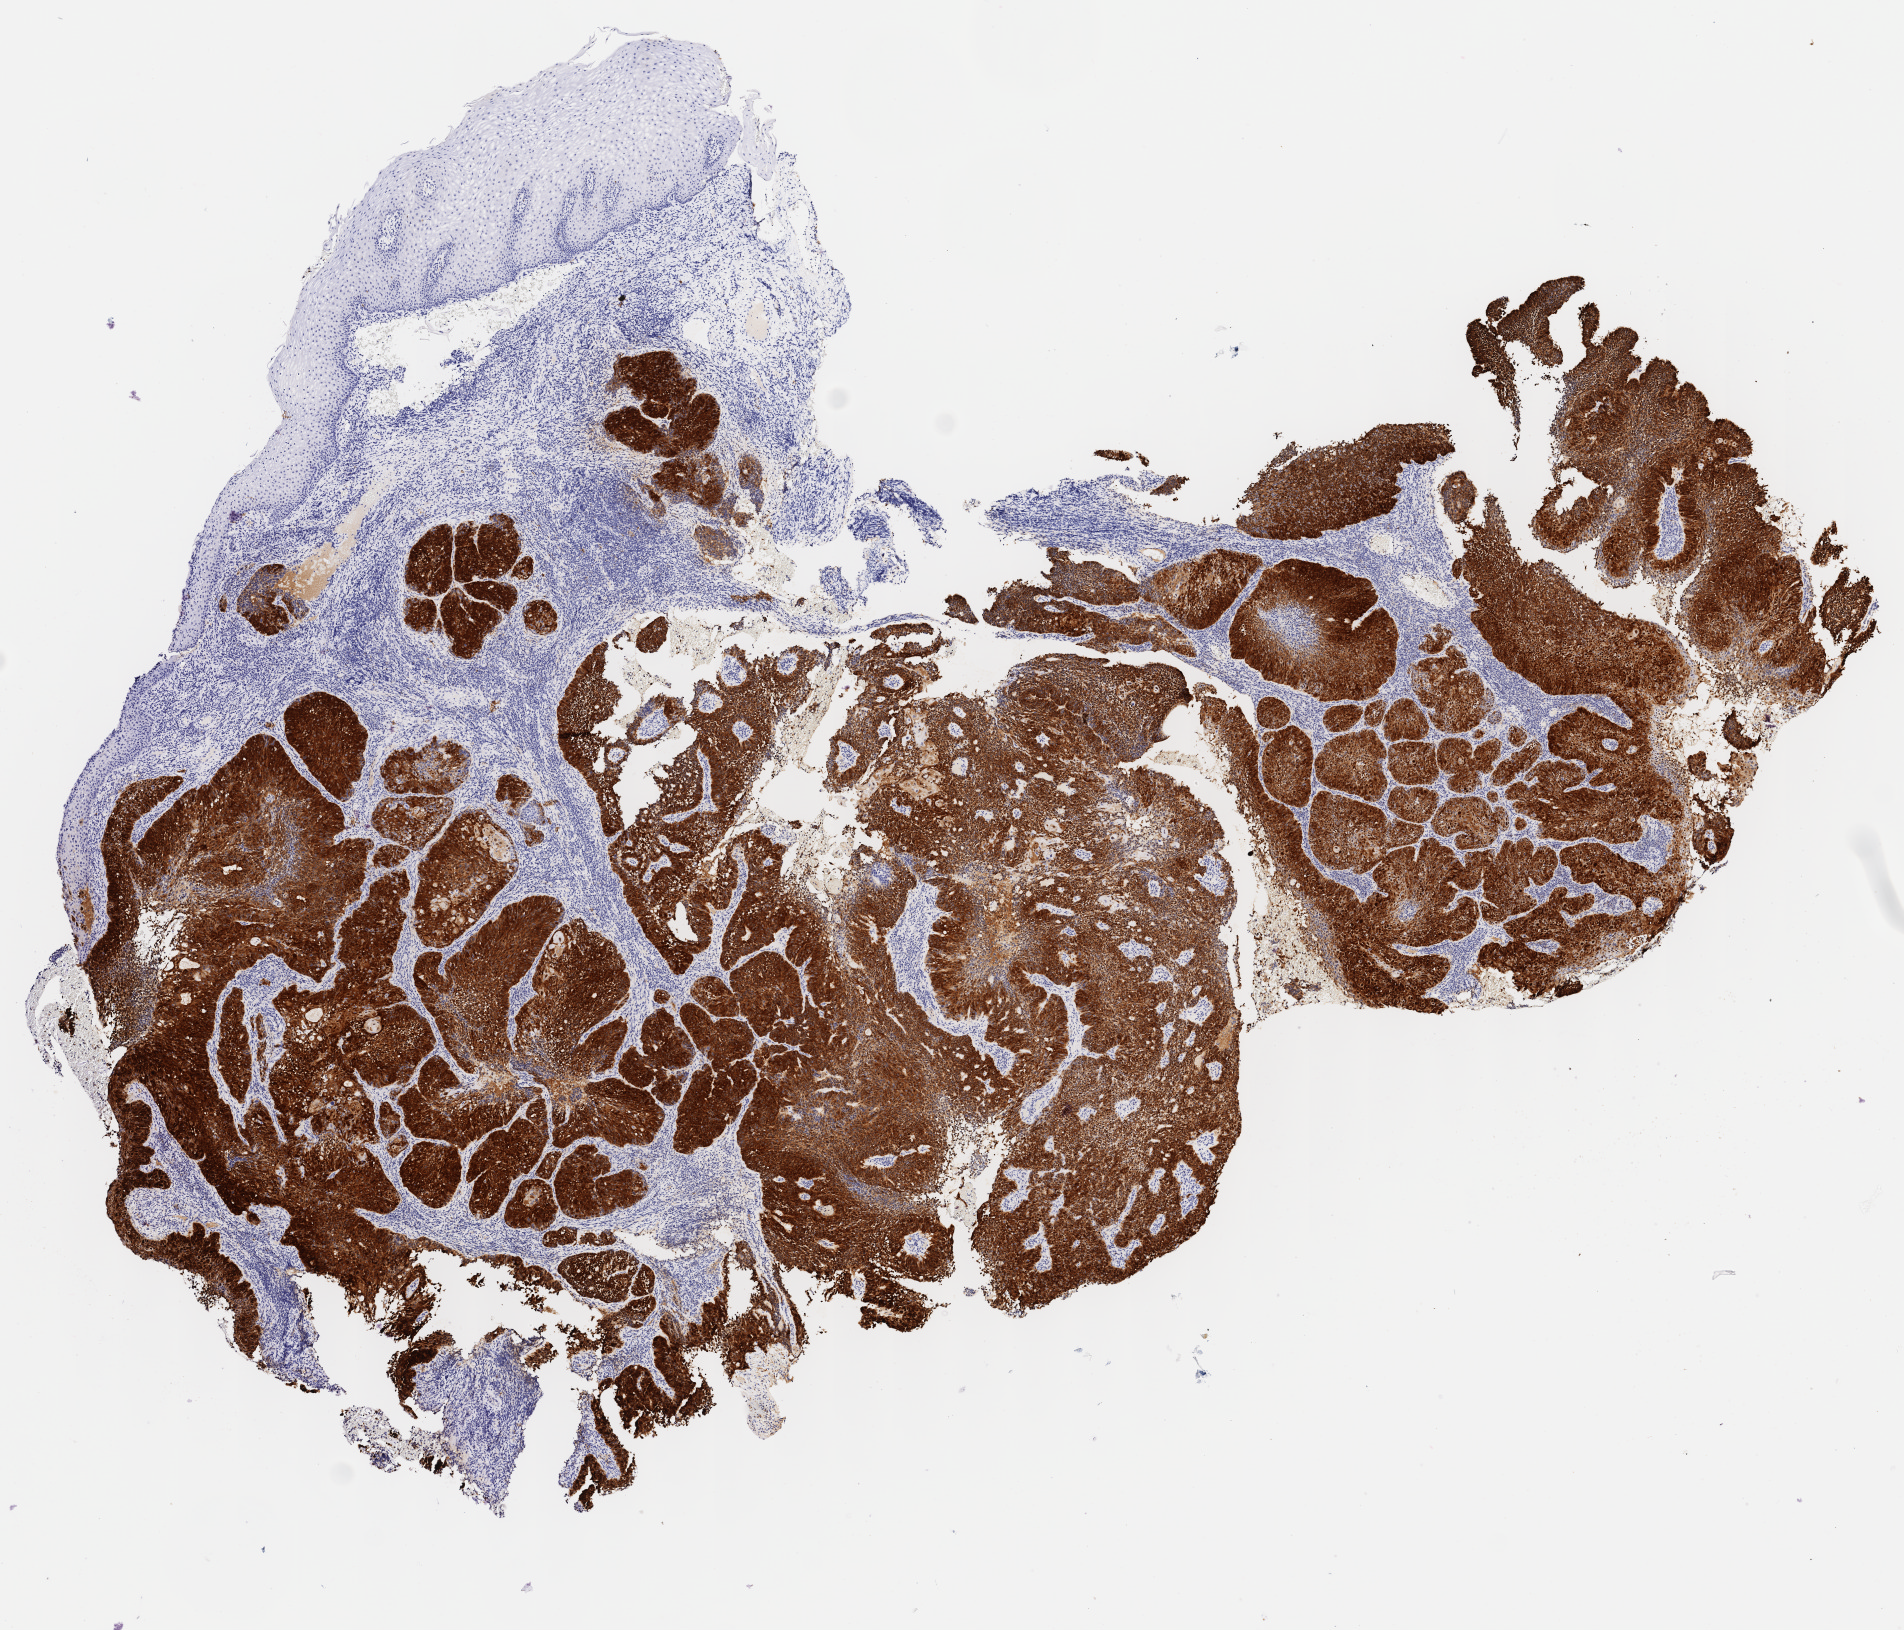
Immunohistochemistry (IHC) whole-slide image stained for p16 (p16INK4a) — shown as a low-resolution overview of the whole scanned area (about 7.6 x 6.5 mm), specimen: tumor tissue, anatomic site: cervix. Patient female; 63 years old.
Histologic diagnosis: Squamous cell carcinoma, large cell, nonkeratinizing, NOS.